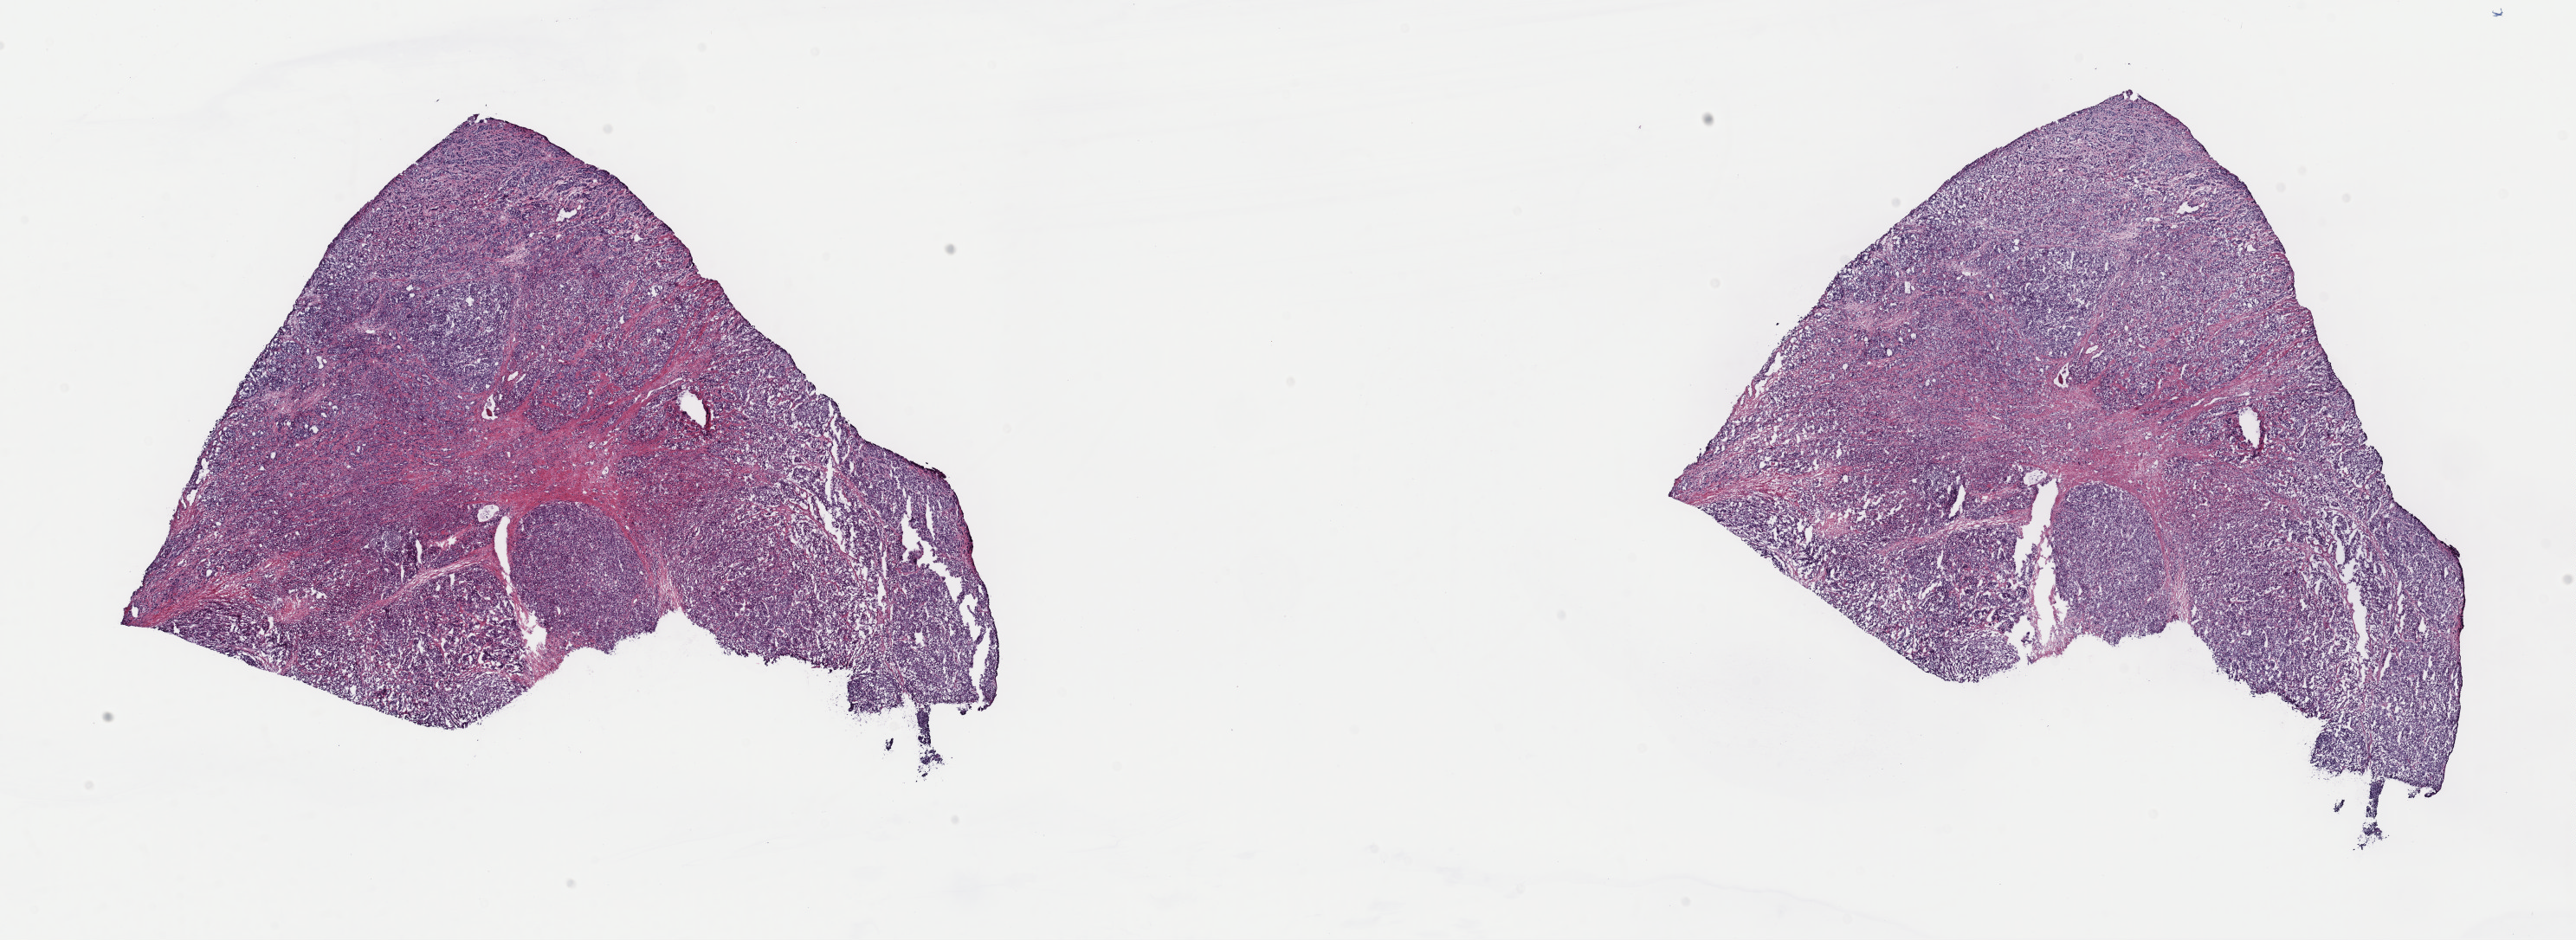
Whole-slide histology image, H&E-stained — whole scanned area (about 23.5 x 8.6 mm, from a 40x scan) shown as a low-resolution overview. Frozen section from the top of the tissue portion. Primary tumour sample from the prostate. Patient: male, age at initial diagnosis 72 years. Gleason score: 9 (4+5). Slide review estimates, as recorded: tumour cells 100%, tumour nuclei 80%, normal cells 0%, stromal cells 0%, necrosis 0%. Inflammatory infiltration, as recorded: lymphocyte infiltration 2%, monocyte infiltration 0%, neutrophil infiltration 0%.
* histologic diagnosis: Adenocarcinoma, NOS (prostate gland)